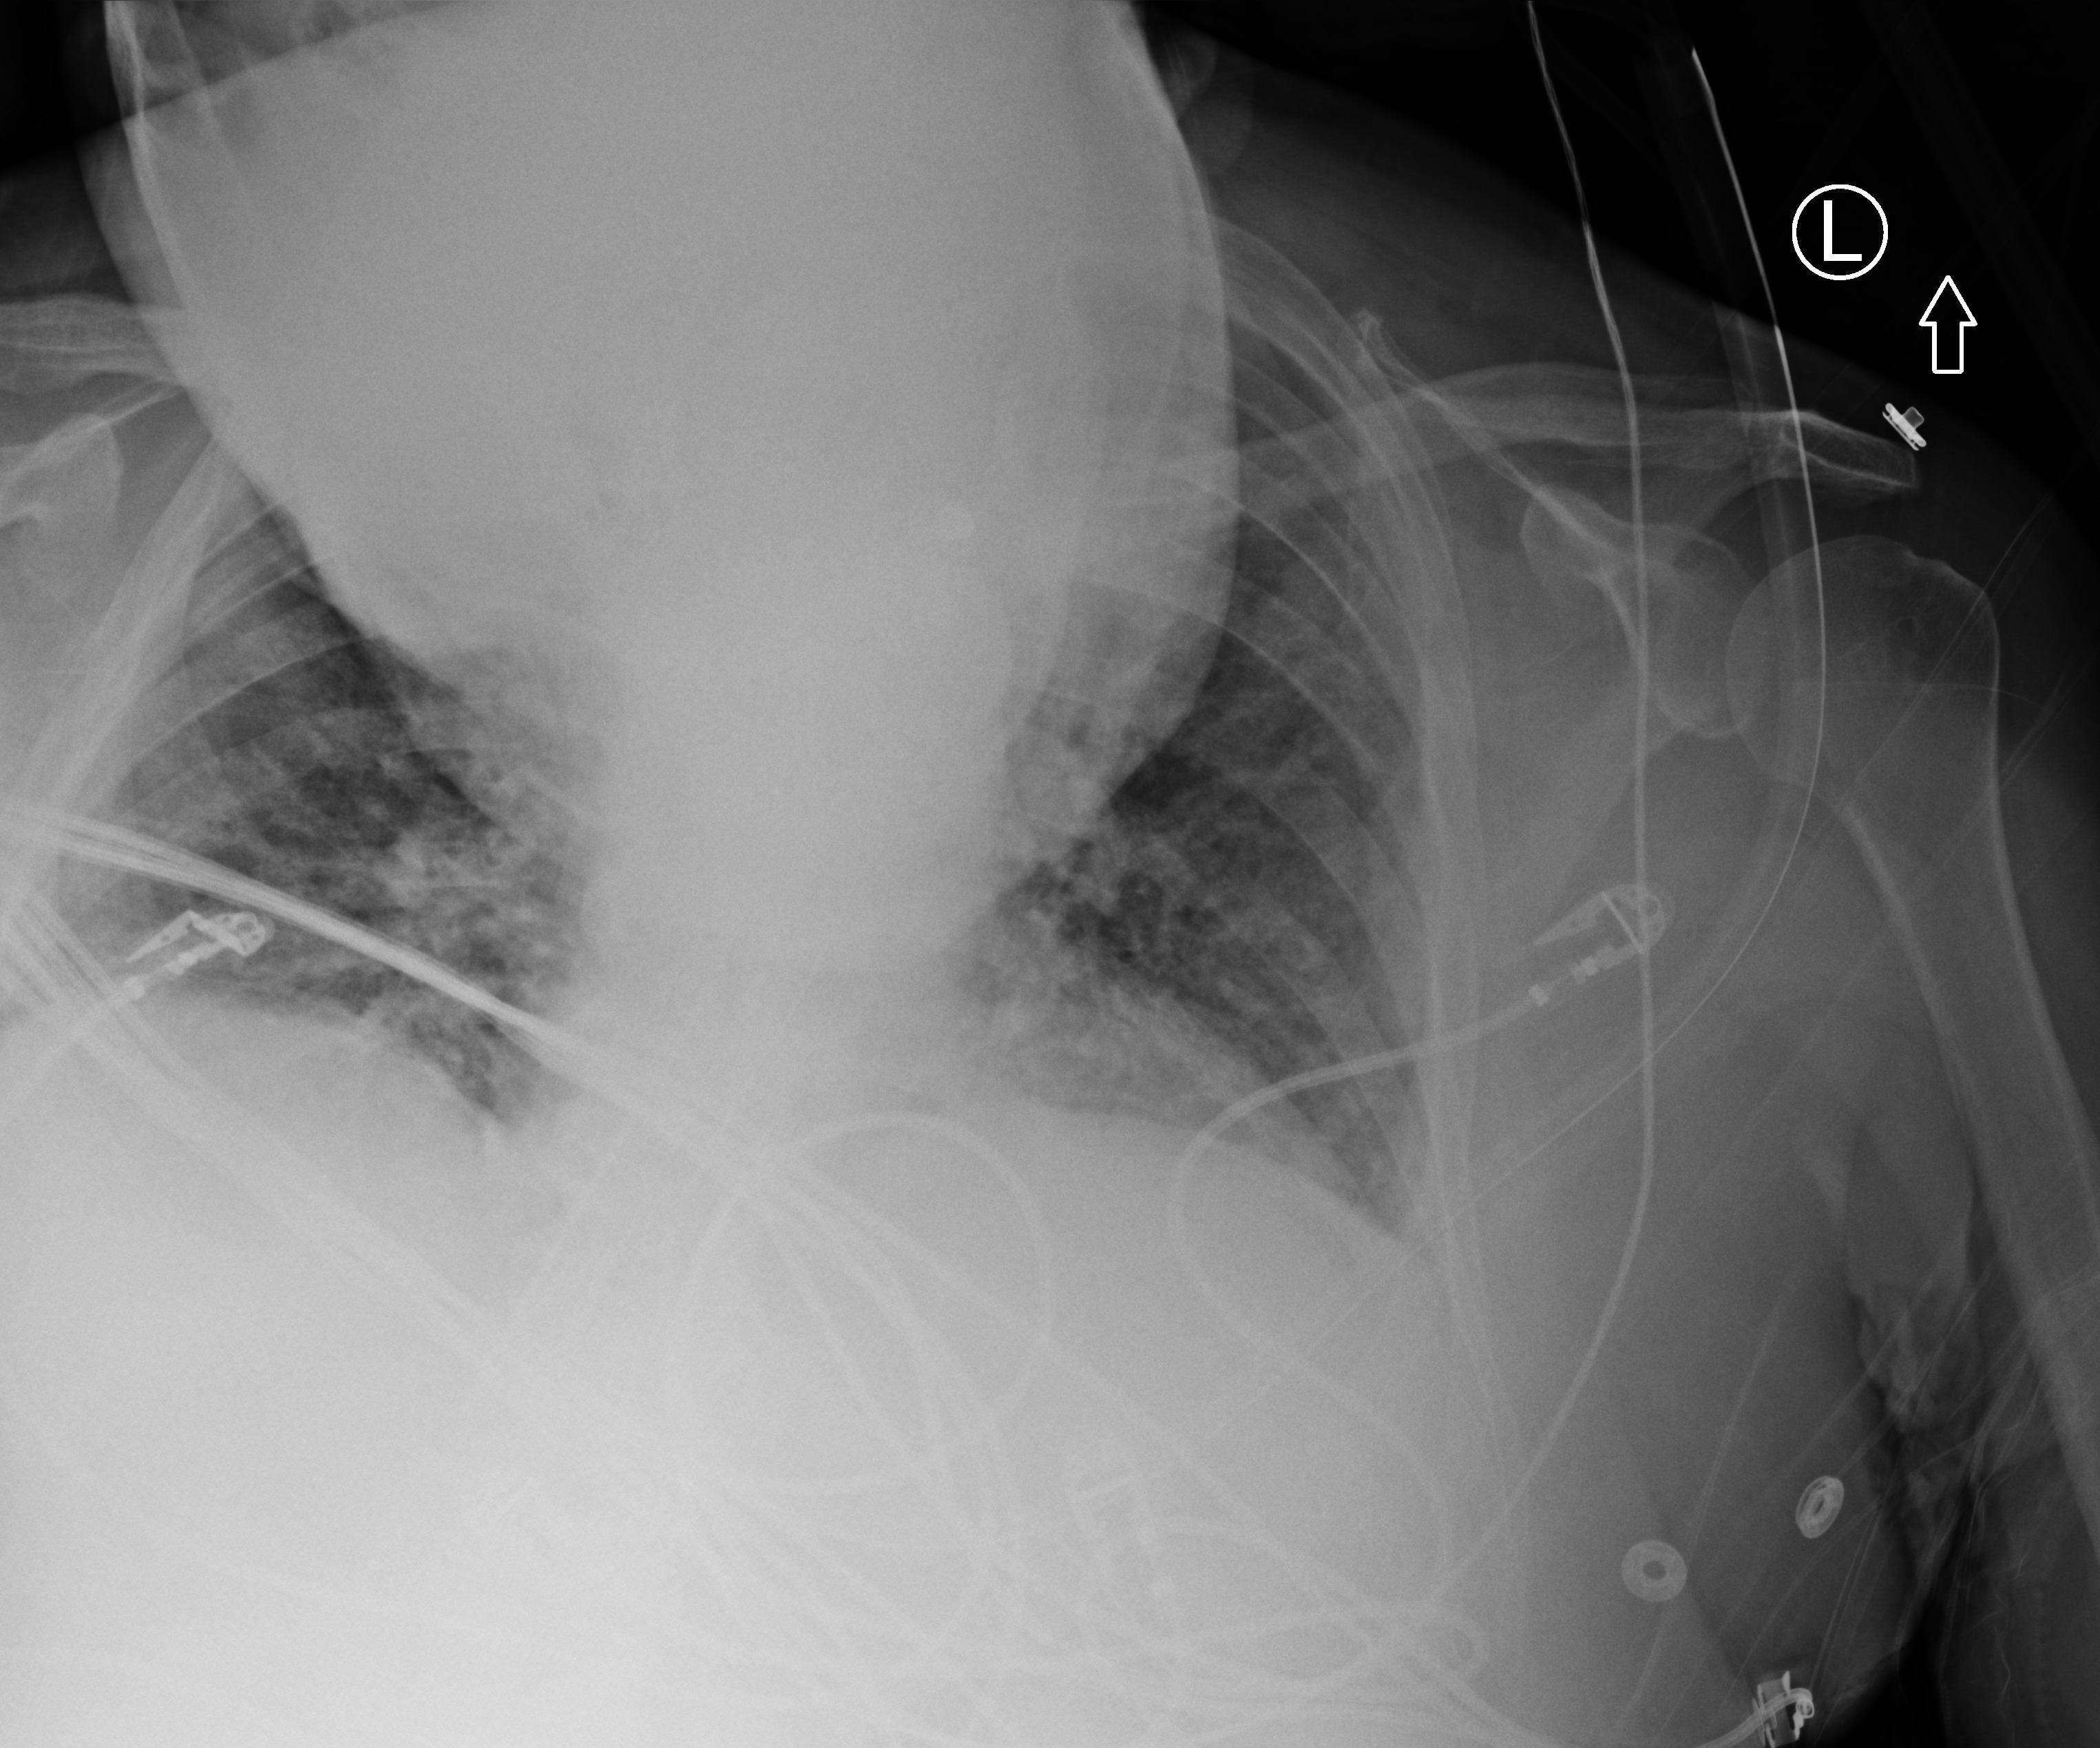
Portable chest radiograph. Male patient hospitalised with COVID-19, age 60–74 years.
From the hospital-stay record, not from the radiograph (when in the stay this image was taken is not recorded): length of hospital stay: 26 days.